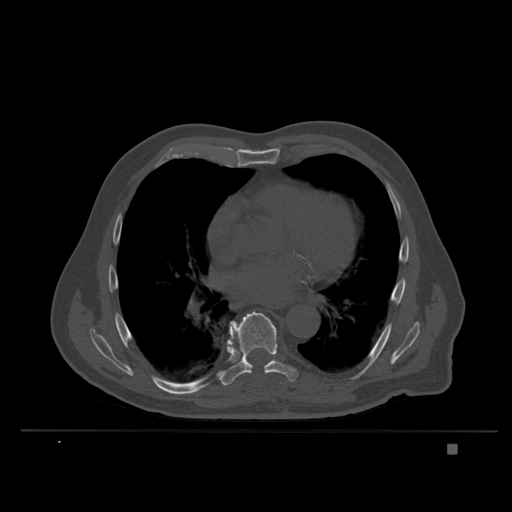
CT including the spine, one axial slice. Position 231 of 435 along the scan axis. Bone window (W 1800 / L 400 HU). 1.5 mm slice thickness. 512 × 512 image matrix, field of view 434 × 434 mm. Male patient, age 73 years. Case-level facts recorded for this patient, not image findings: primary cancer: skin.
Annotated regions visible in this slice (semi-automatically segmented with operator editing):
- T7 vertebra: bounding box (x1, y1, x2, y2) in pixels: (228, 324, 237, 342)
- T8 vertebra: (219, 311, 299, 386)